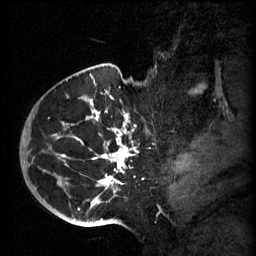
Breast MRI (dynamic contrast-enhanced), one sagittal slice; slice 46 of 60 in the series (ordered by position); 3 images stored at this slice position (order not interpretable as contrast timing); 1.5 T; TE 4.2 ms, TR 11 ms; 256 × 256 image matrix, field of view 200 × 200 mm. Female patient, age 51 years.
Annotated regions visible in this slice (semi-automatic segmentation, software-assisted and operator-edited):
- analysis volume of interest (the breast-tissue region the enhancement analysis was run in; not a lesion): bounding box <48,82,153,197> (left, top, right, bottom; pixels)
- tumour enhancement mask (voxels above the 70 % enhancement threshold inside the analysis volume of interest): <85,92,134,193>